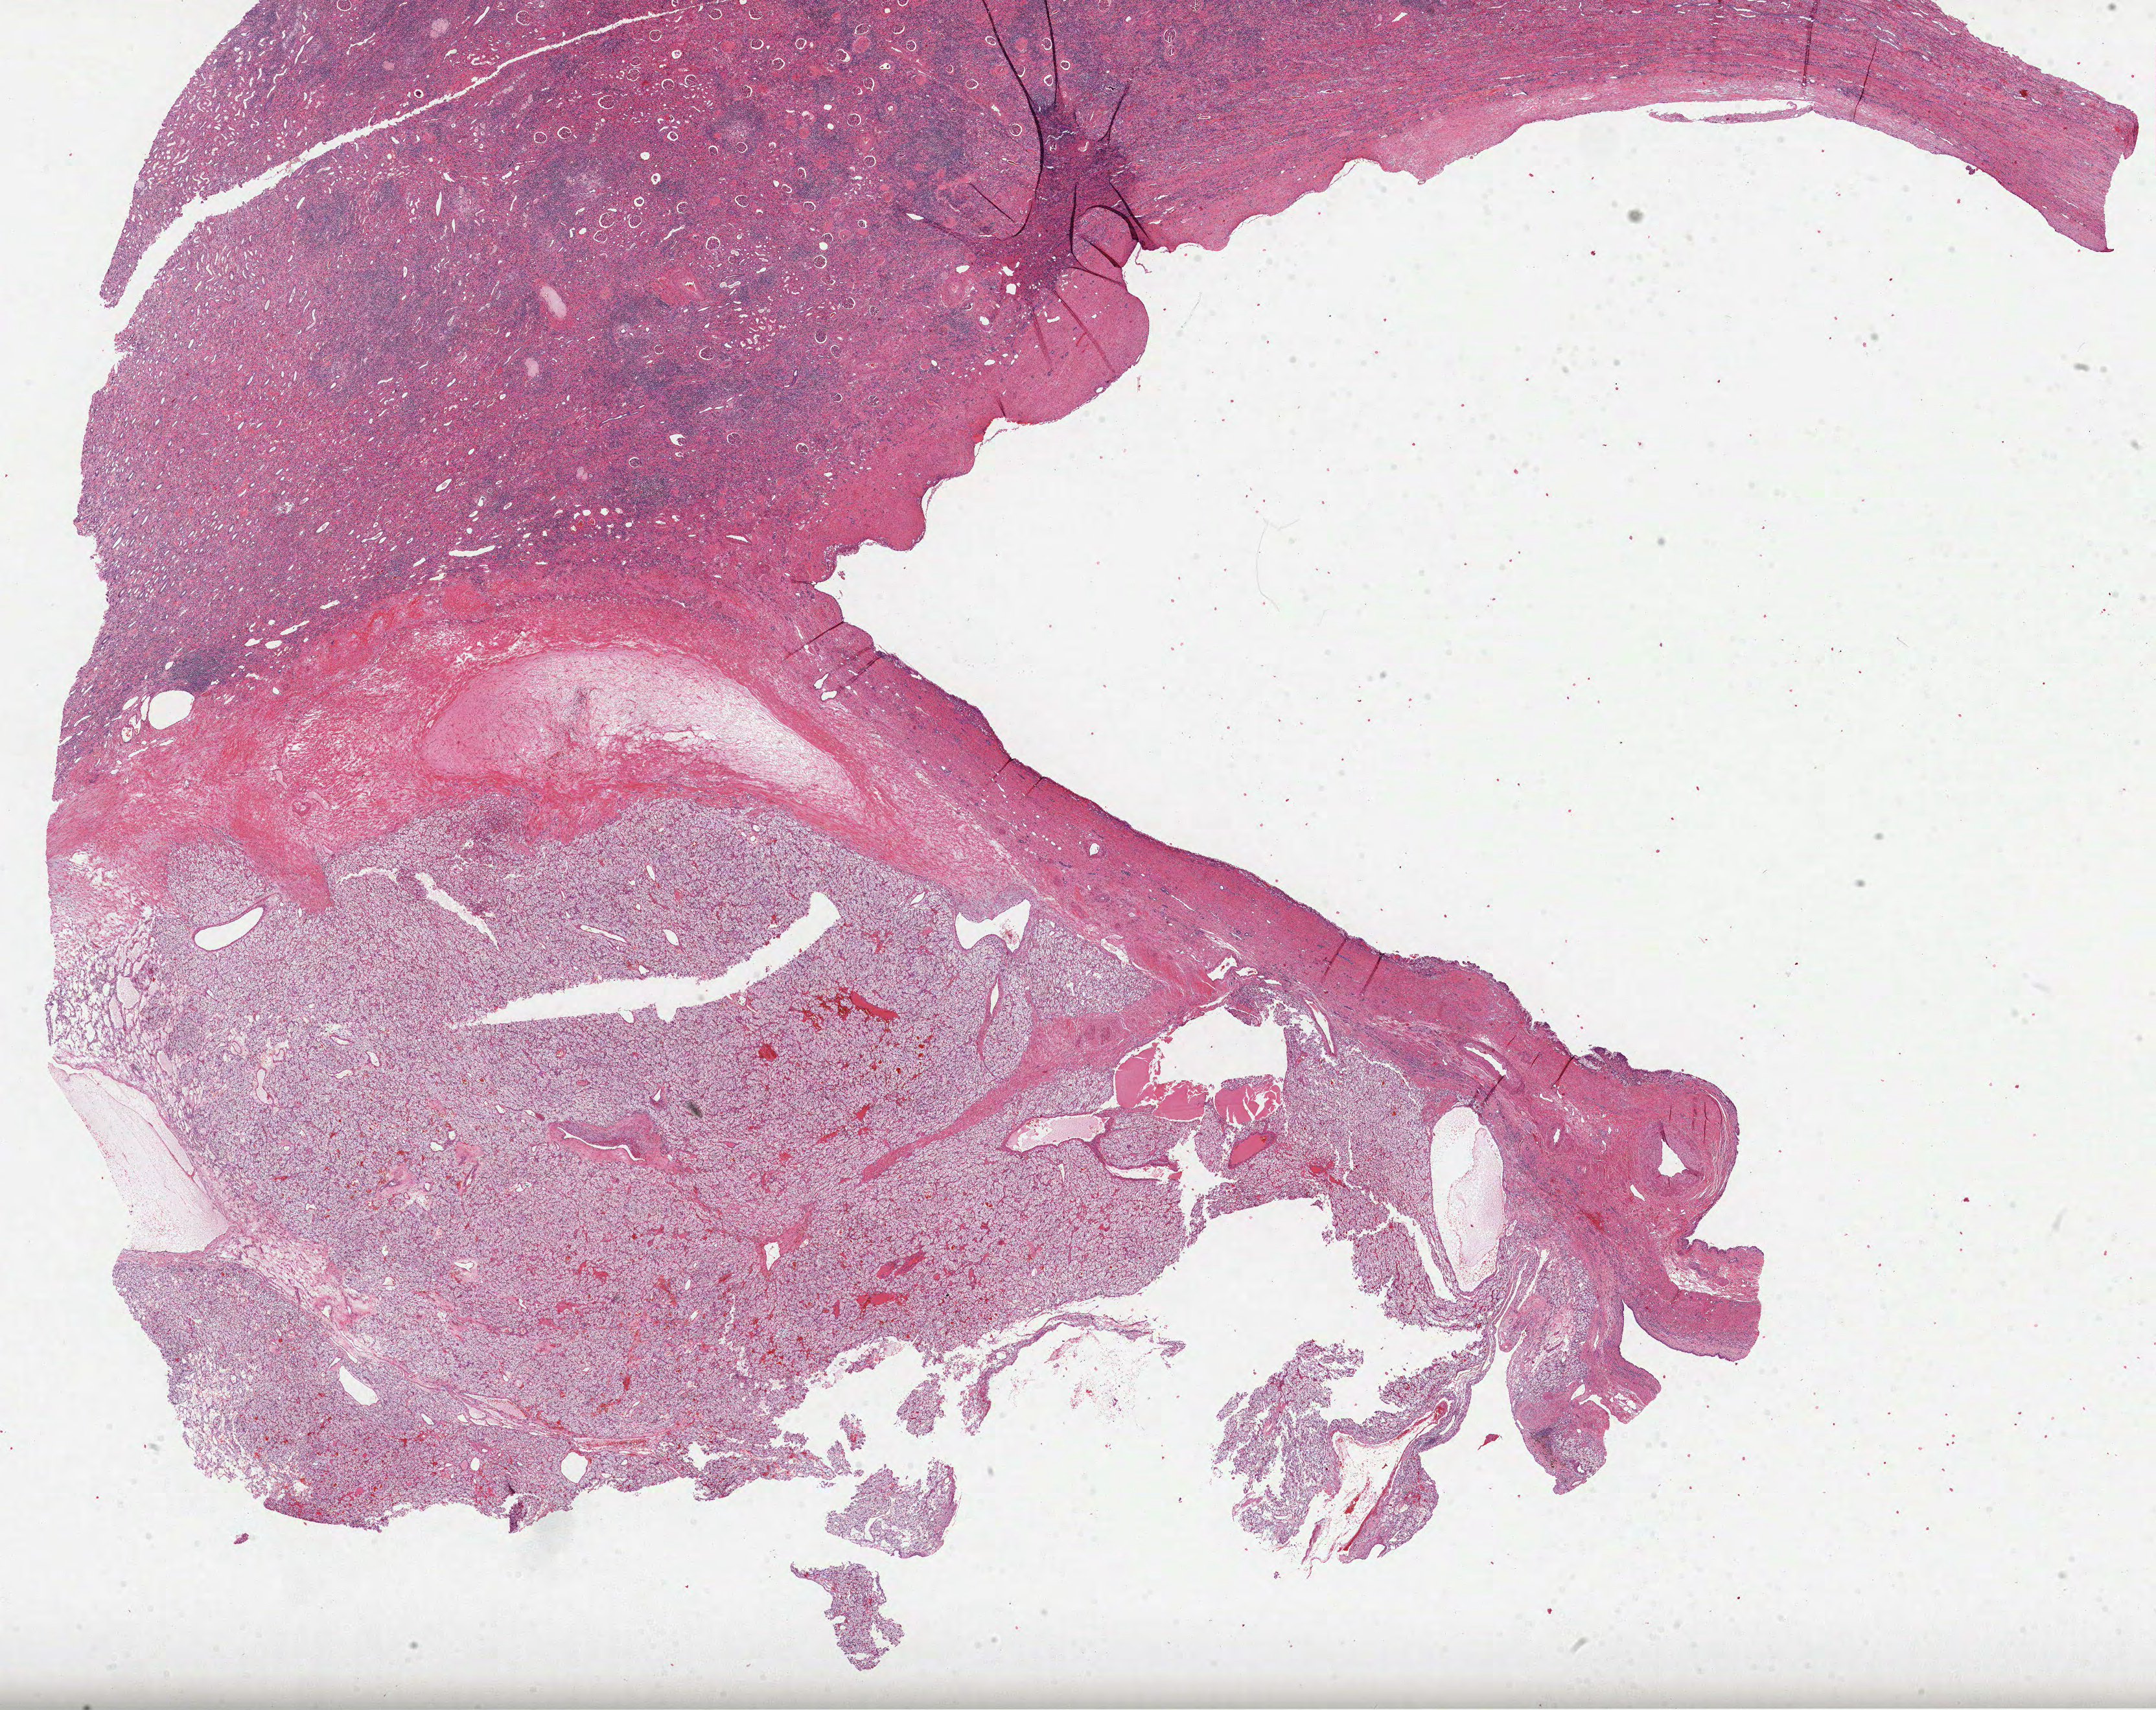
Whole-slide histology image, H&E-stained — shown as a low-resolution overview of the whole scanned area (about 26.8 x 21.3 mm). FFPE section. Kidney, primary tumour sample. Female patient; age at initial diagnosis 47 years. Histologic grade: G2 (moderately differentiated).
* AJCC pathologic stage: I (6th edition)
* diagnosis: Clear cell adenocarcinoma, NOS